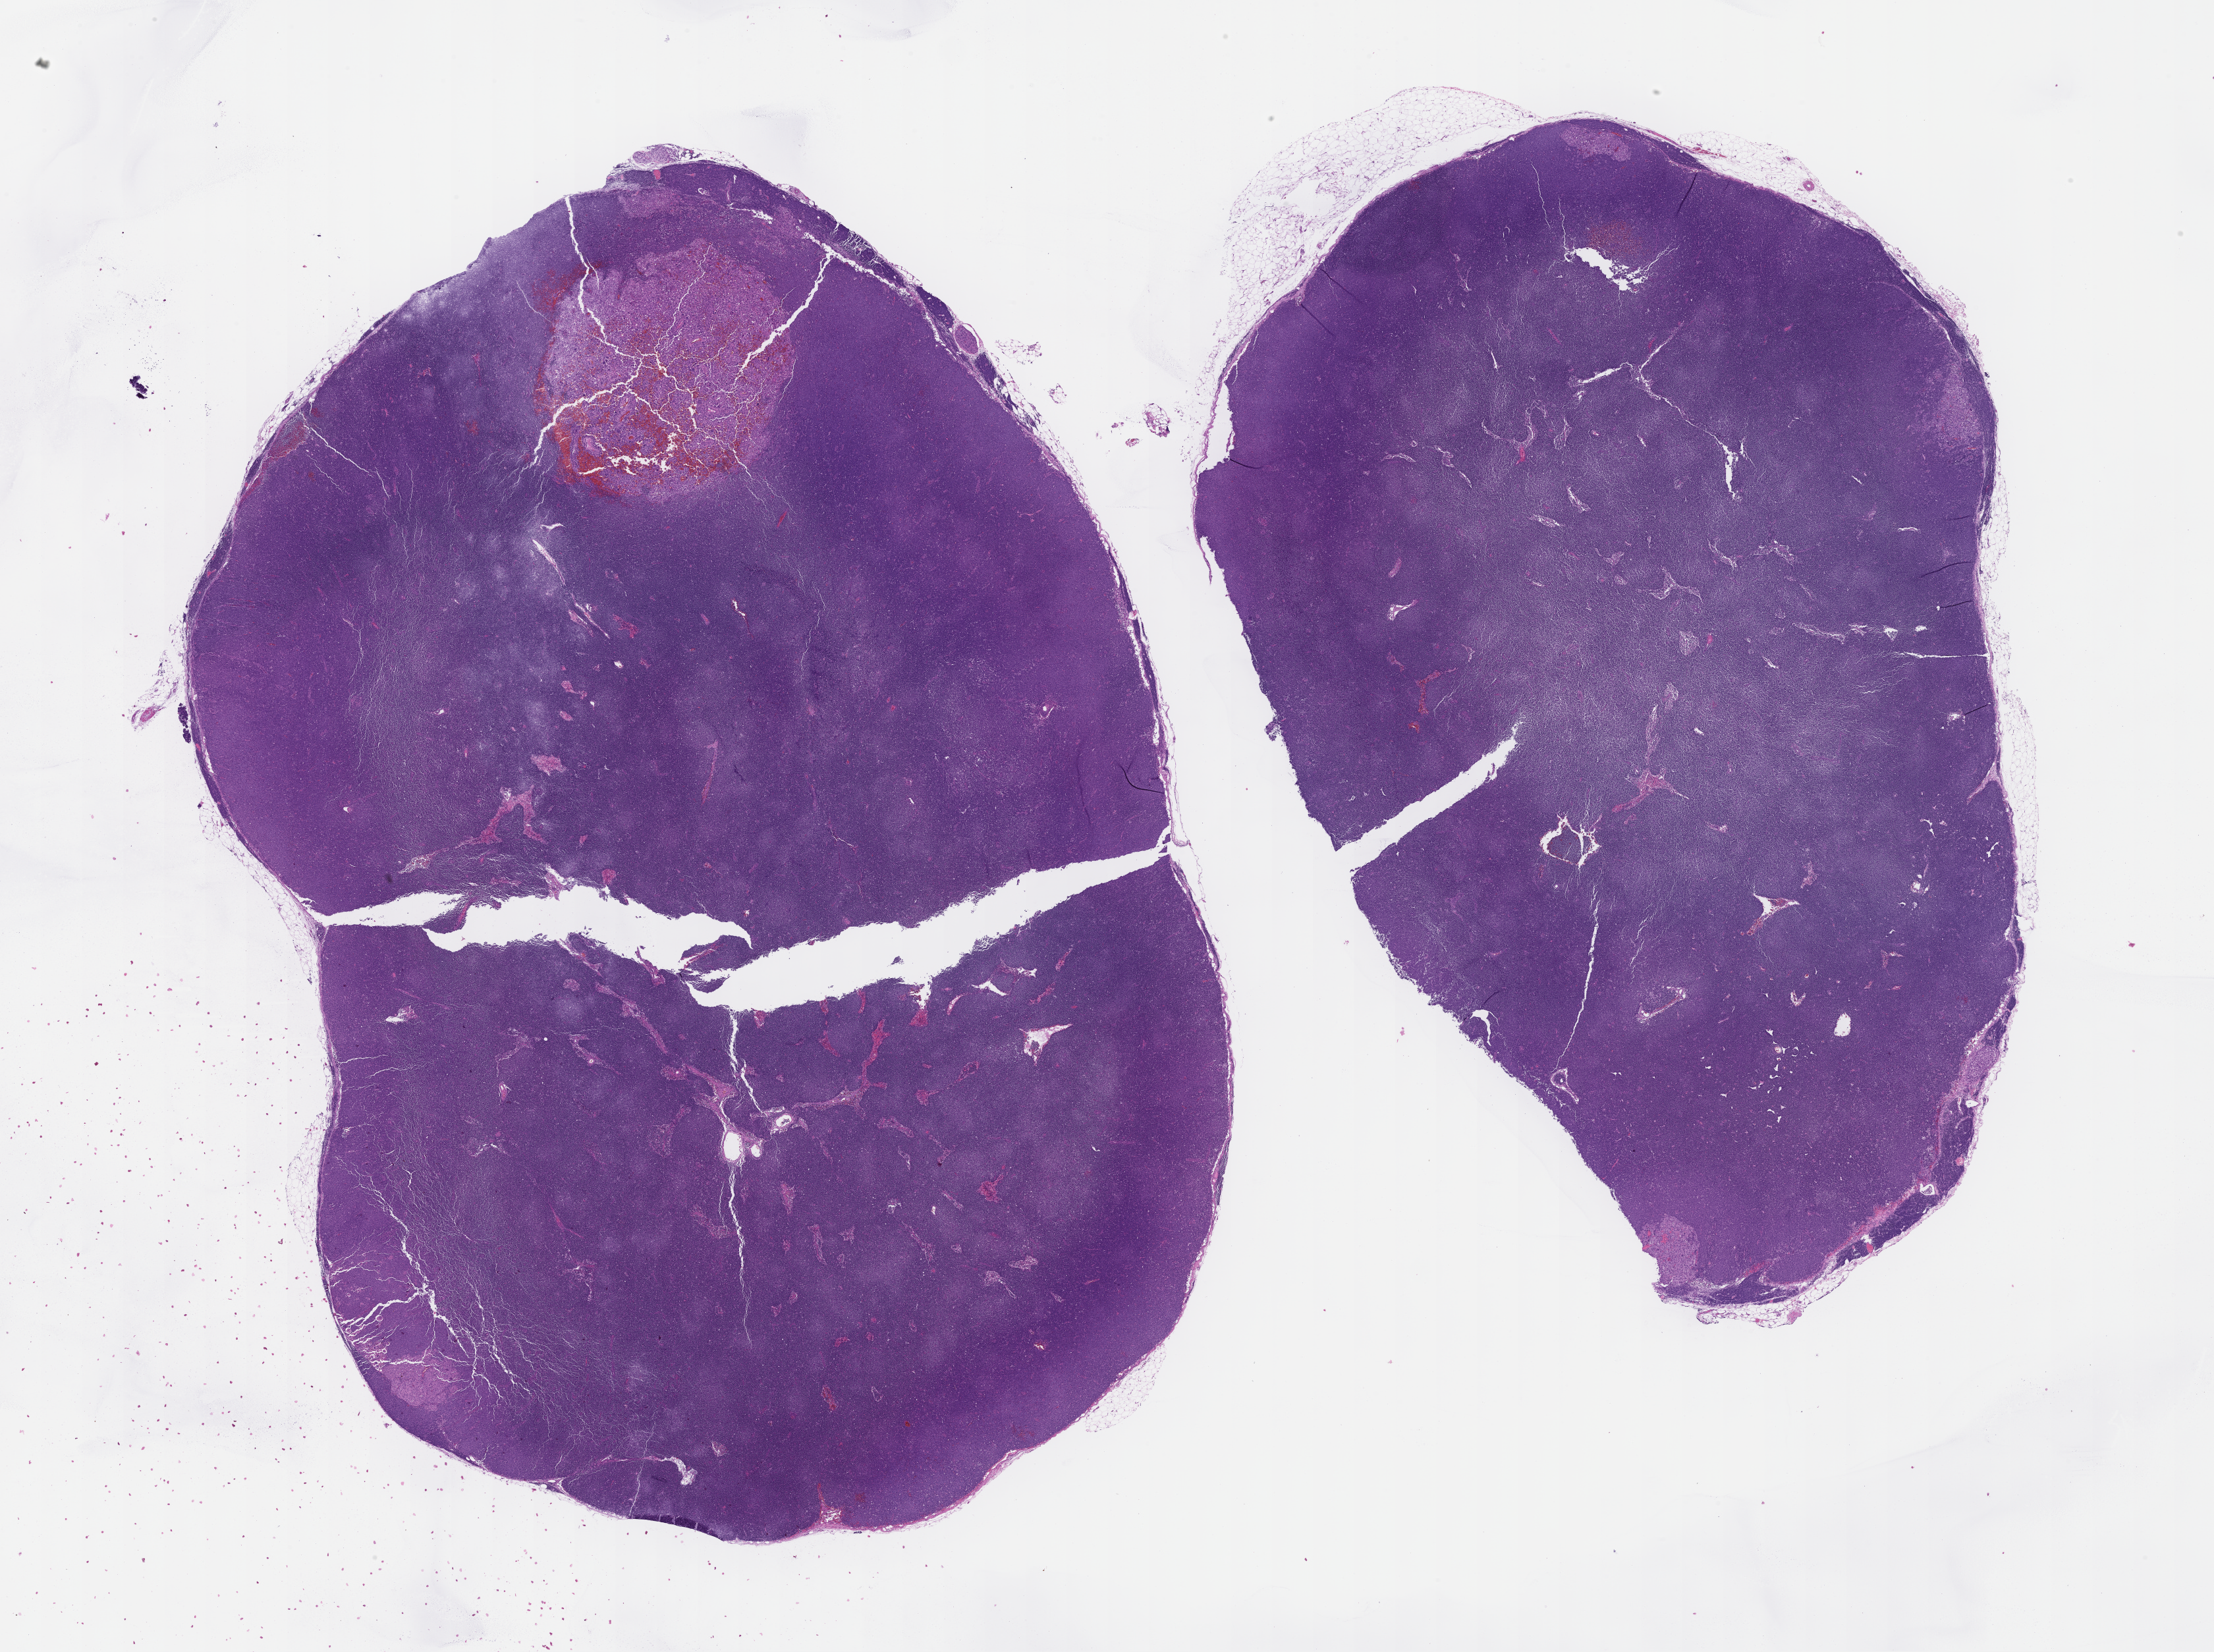
Hematoxylin and eosin (H&E) whole-slide image, a low-resolution overview of the entire scanned area, about 27.1 x 20.3 mm; FFPE section; tissue site: skin. Patient sex: female.
This section: primary tumour tissue. Diagnosis: Melanoma.